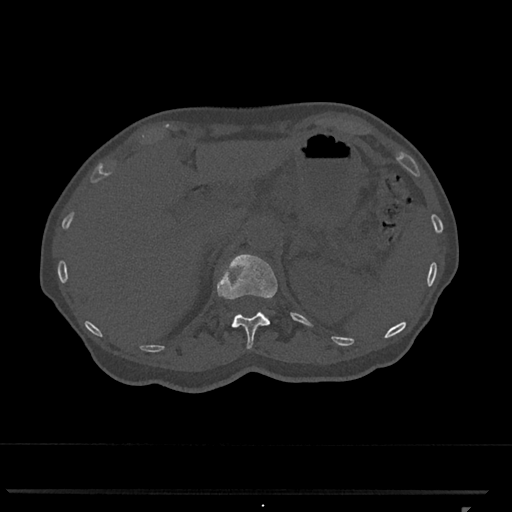
CT including the spine, one axial slice; position 449 of 793 along the scan axis; reconstruction kernel Br40s/3; 120 kVp; bone window (W 1800 / L 400 HU); 0.5 mm slice thickness; 512 × 512 image matrix, field of view 380 × 380 mm. Female patient, age 62 years. Case-level facts recorded for this patient, not image findings: primary cancer: renal.
Structures marked on this image (semi-automatically segmented with operator editing):
- T12 vertebra: bounding box <217,254,278,349> (left, top, right, bottom; pixels)